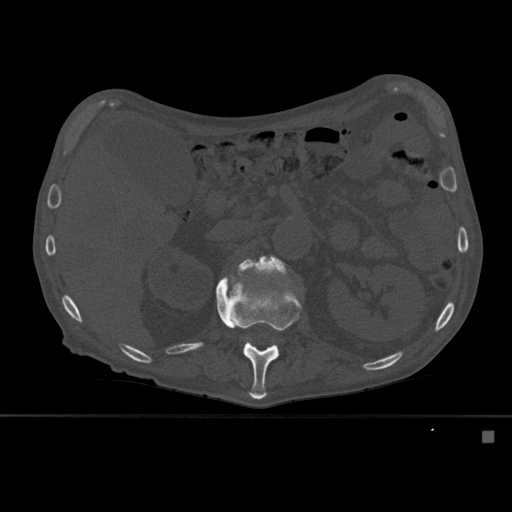
CT including the spine, one axial slice. Position 251 of 527 along the scan axis. Bone window (W 1800 / L 400 HU). 1.5 mm slice thickness. 512 × 512 image matrix, field of view 373 × 373 mm. Patient: male, 78 years. From the clinical record (not read from this slice): primary cancer: prostate.
Outlined on this slice (semi-automatically segmented with operator editing):
- L1 vertebra: bounding box (x1, y1, x2, y2) in pixels: (216, 277, 301, 400)
- L2 vertebra: (237, 255, 287, 276)